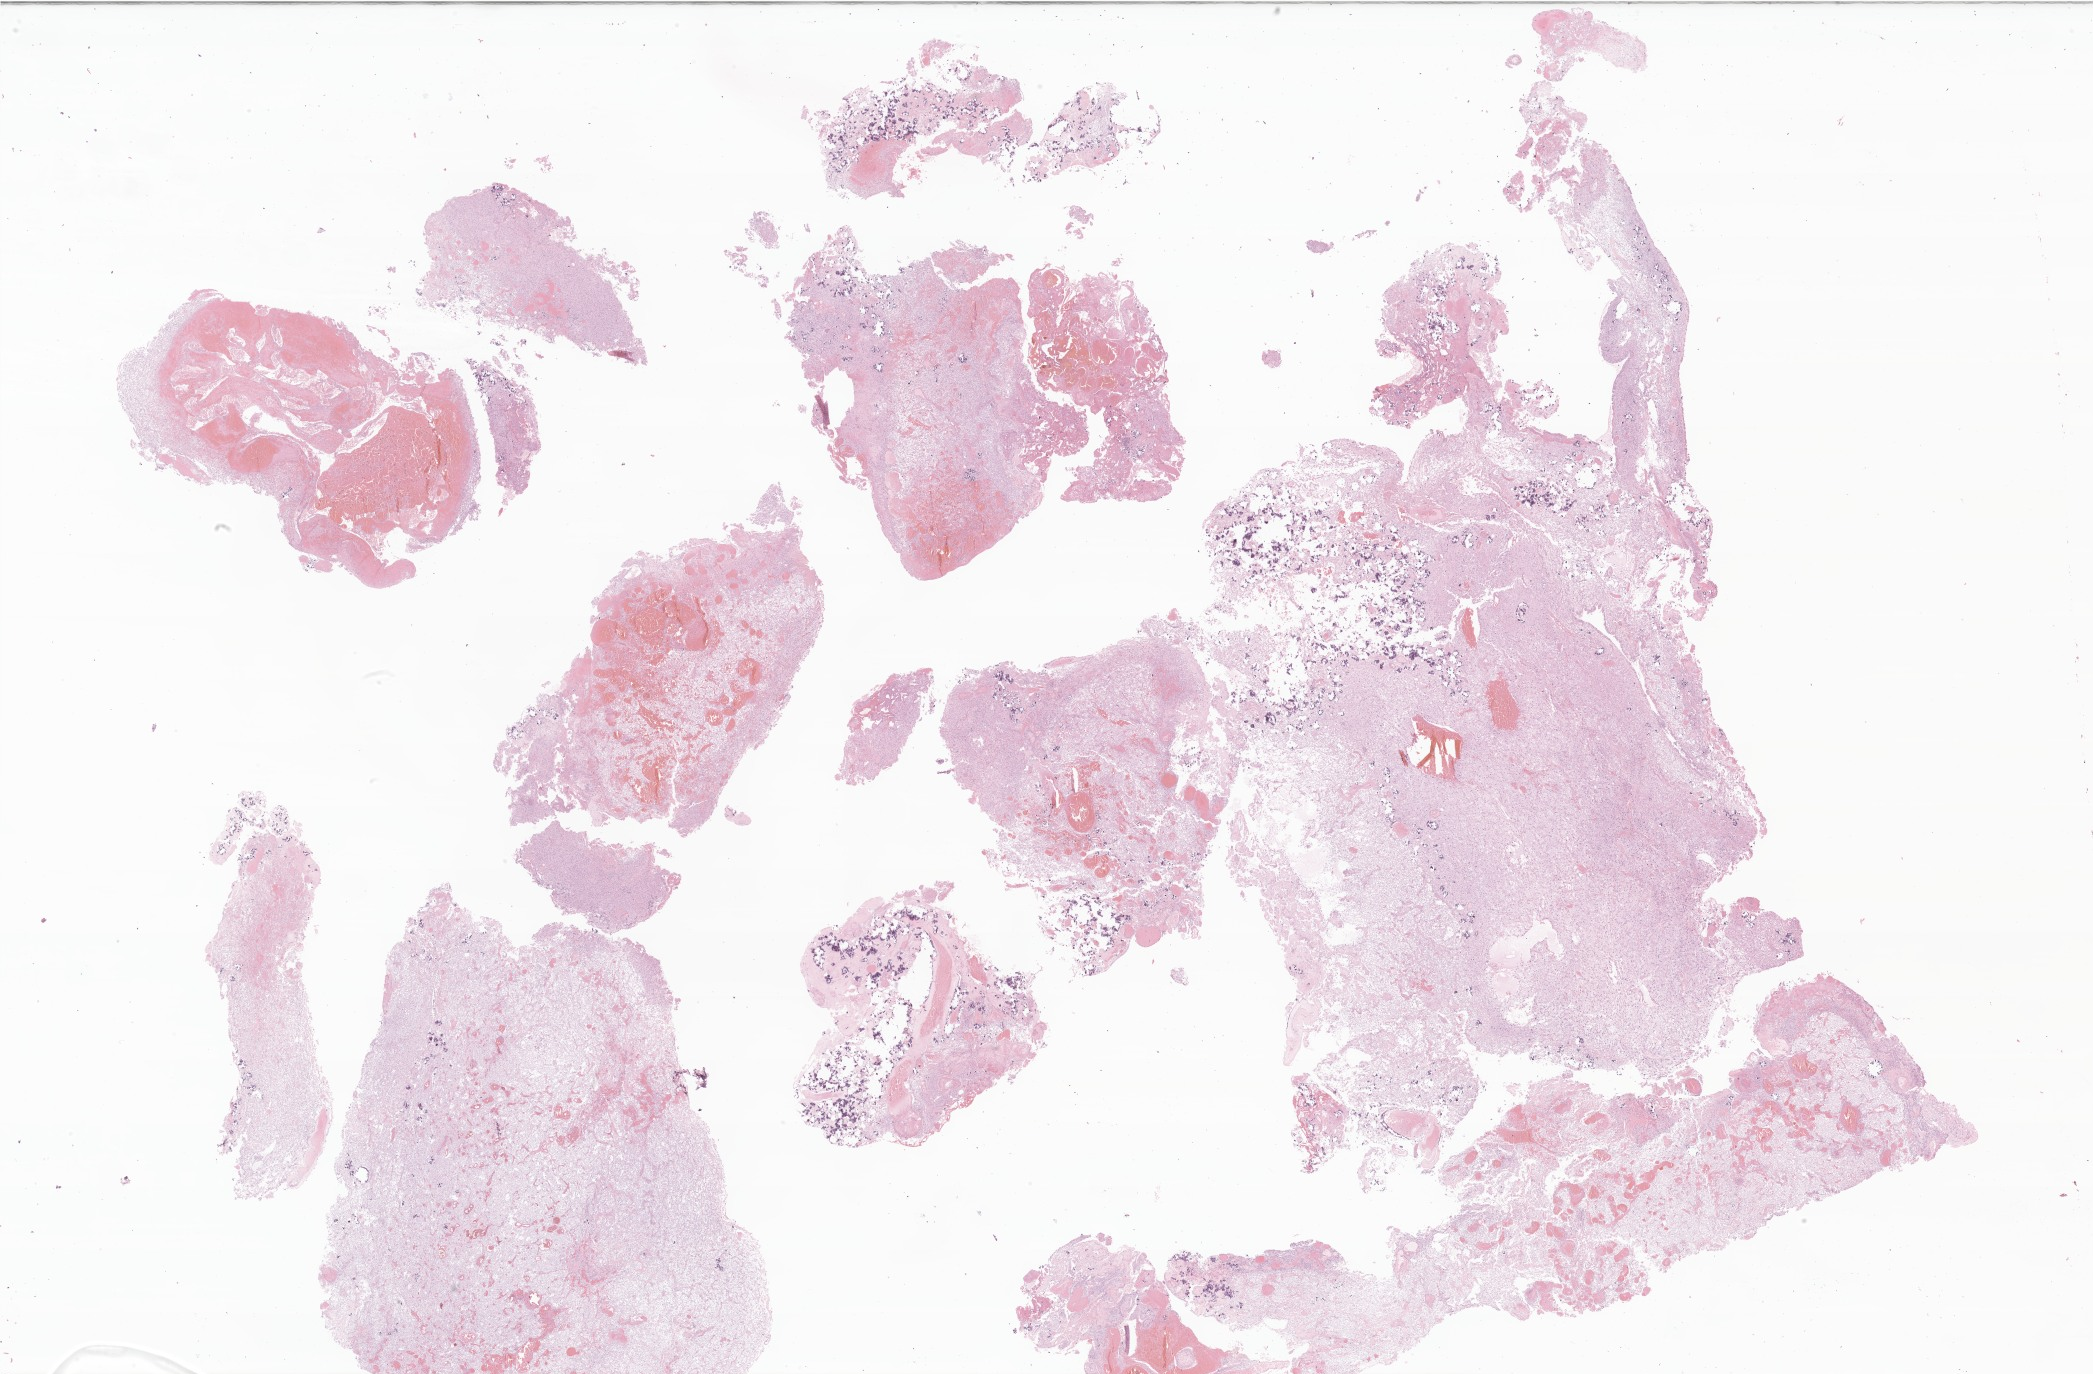
Whole-slide image, haematoxylin and eosin stain of tumor tissue from the brain — shown as a low-resolution overview of the whole scanned area (about 35.3 x 23.2 mm). Formalin-fixed paraffin-embedded section. Female patient, age 150 months.
Diagnosis: Pilocytic astrocytoma.